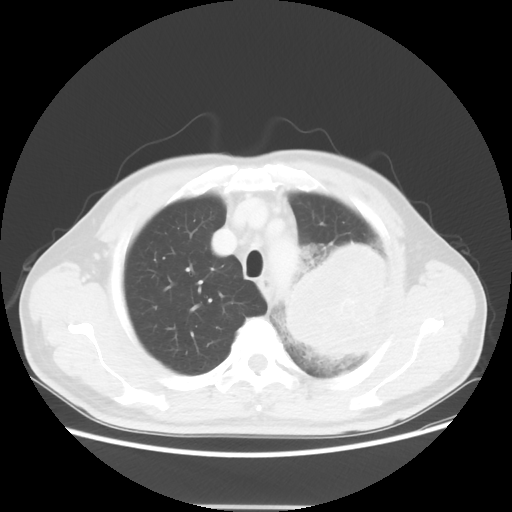
Chest CT, one axial slice. Position 44 of 53 along the scan axis. Reconstruction kernel STANDARD. Lung window (W 1500 / L -600 HU). 5 mm slice thickness. 512 × 512 image matrix. Male patient, age 60 years. From the clinical record (not read from this slice): clinical TNM (as recorded): T4 N1 M1a; histopathological grade: G3.
Annotated regions visible in this slice (rectangle marked by the reading radiologist):
- lung tumour (recorded histology: large cell carcinoma): bounding box (x1, y1, x2, y2) in pixels: (287, 236, 391, 365)